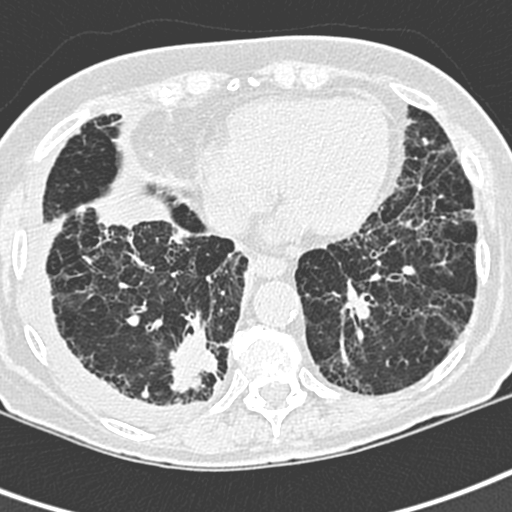
Low-dose screening chest CT, one axial slice; slice 86 of 220 in the series (ordered by position); 120 kVp; lung window (W 1500 / L -600 HU); 1.3 mm slice thickness; 512 × 512 image matrix, field of view 288 × 288 mm.
Outlined on this slice (outlined manually by an expert reader):
- lesion 1 (tumor, lower lobe of right lung): bounding box (x1, y1, x2, y2) in pixels: (169, 345, 218, 393)